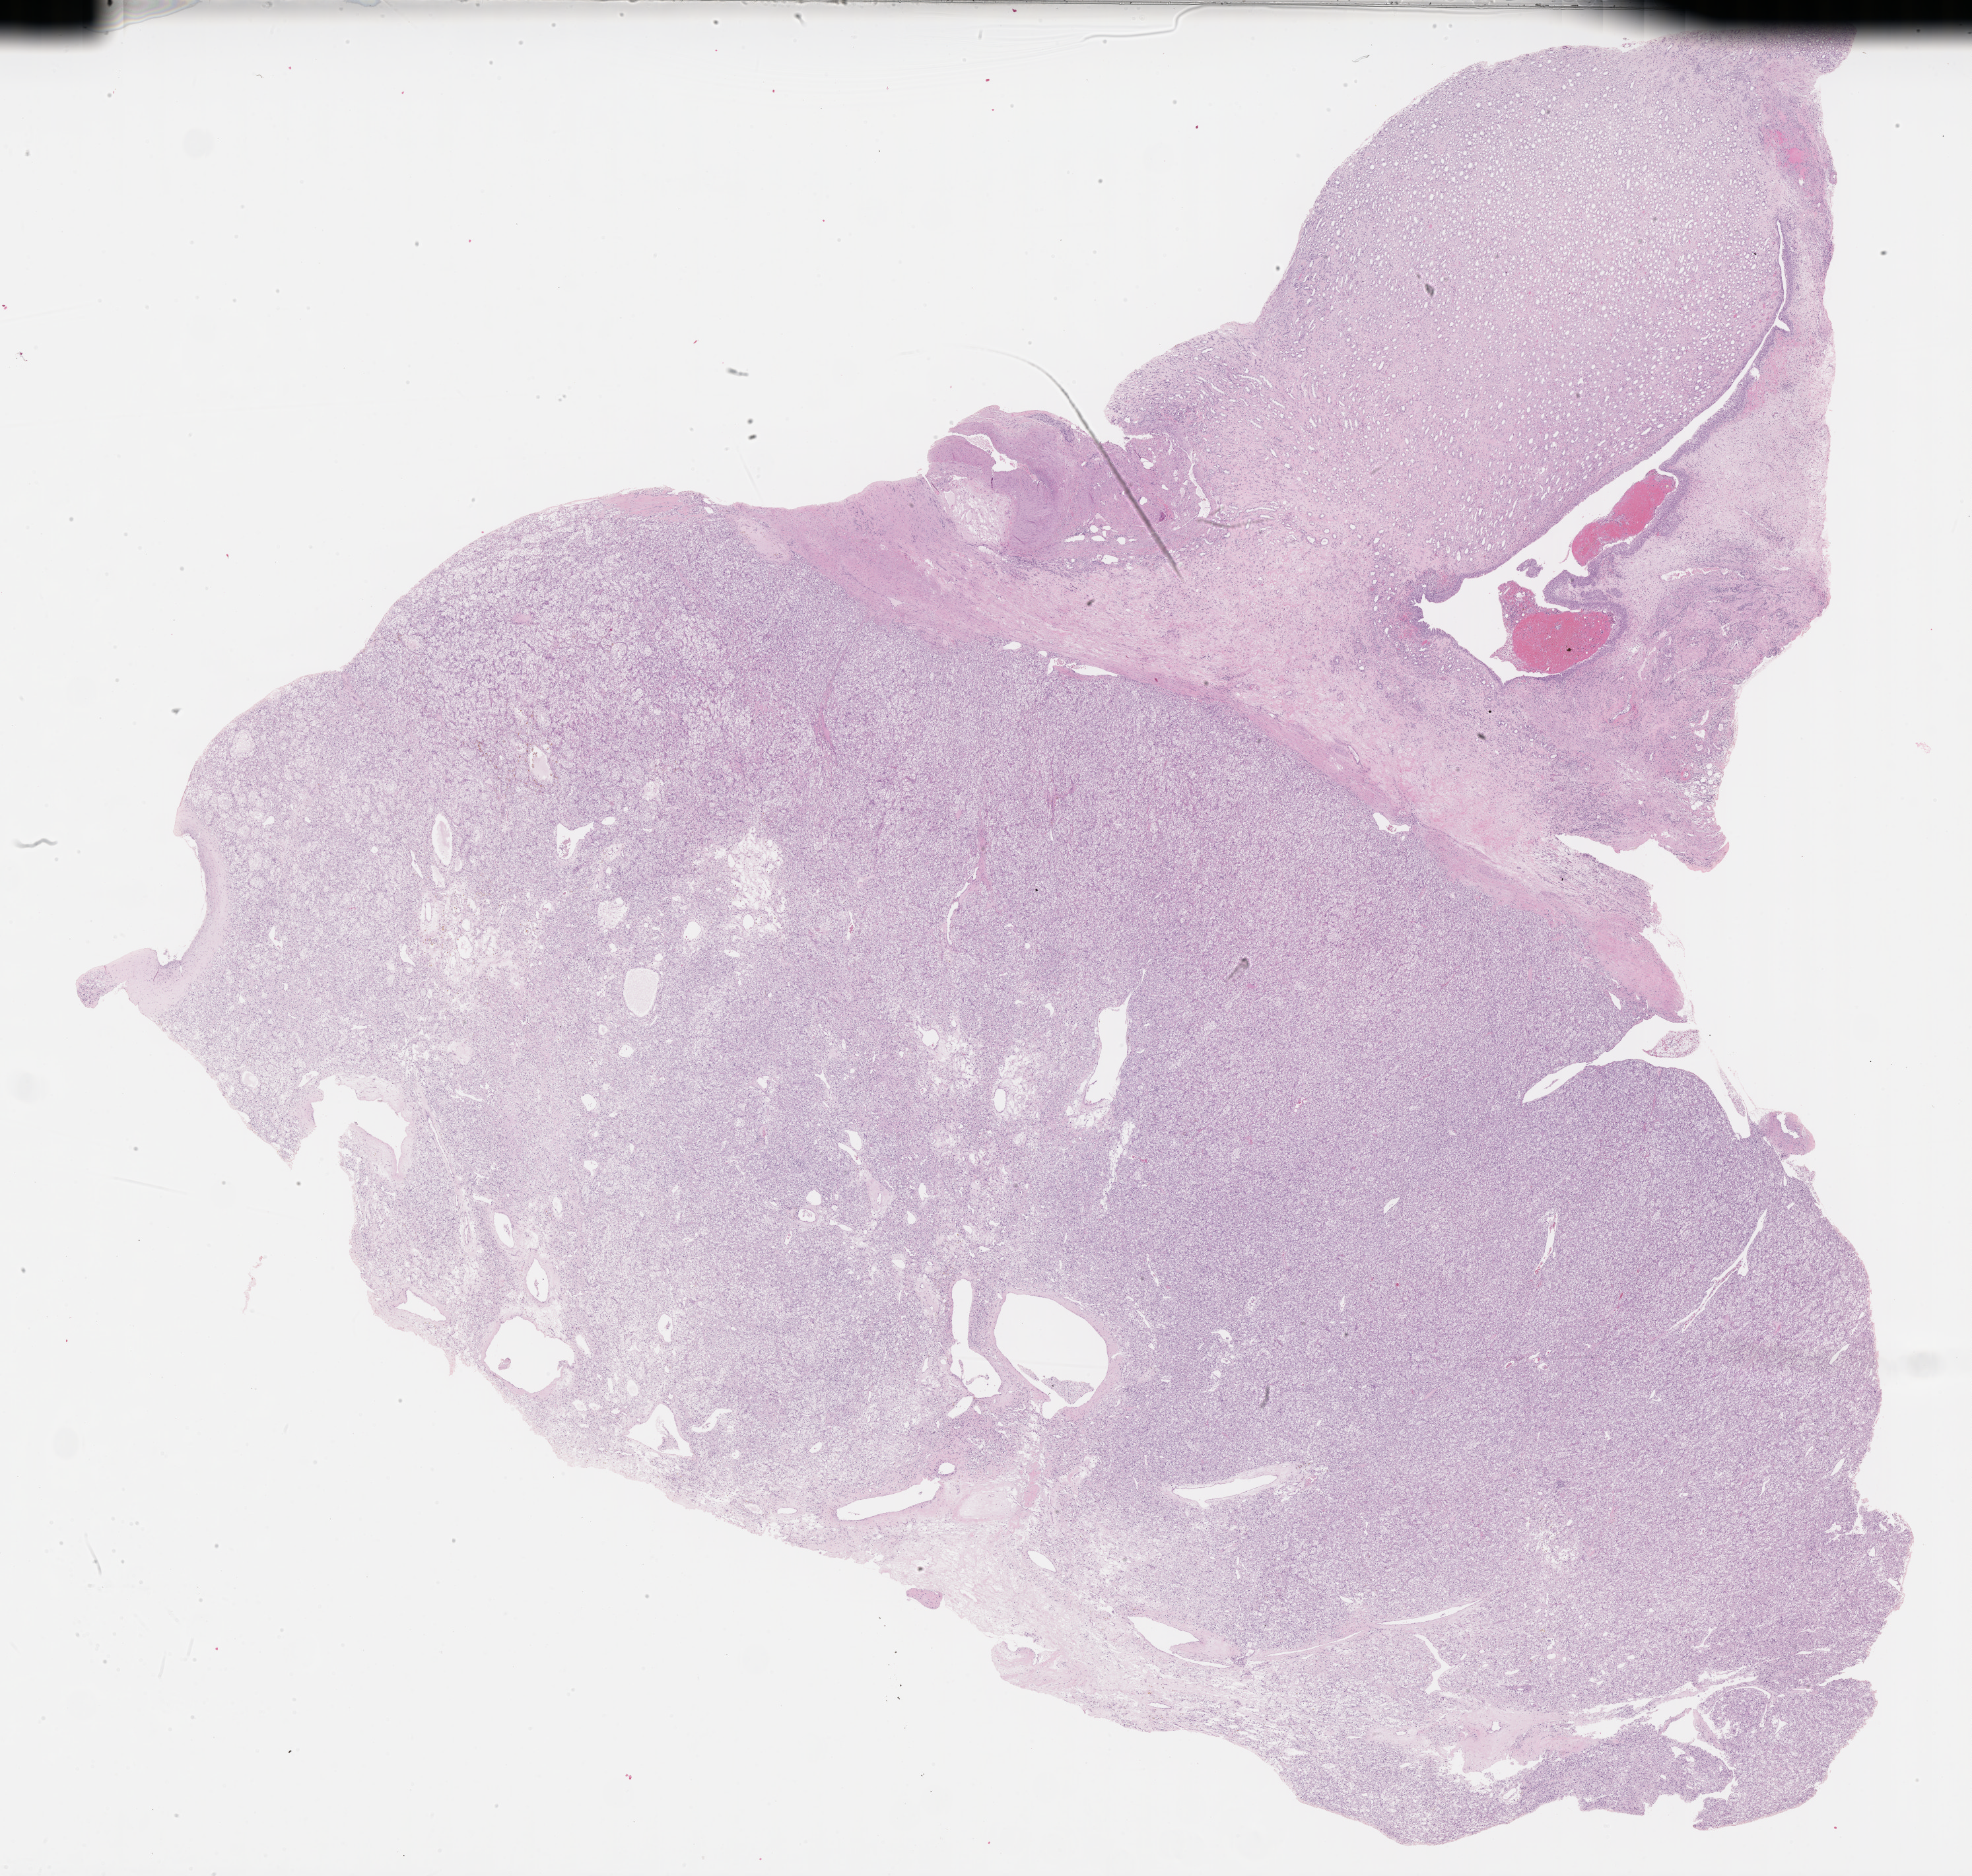
Whole-slide histology image, H&E-stained — low-resolution overview of the scanned area, about 24.2 x 23.0 mm (acquisition: 40x scan). FFPE section. Kidney, primary tumour sample. Male patient; age at initial diagnosis 62 years.
Histologic diagnosis: Clear cell adenocarcinoma, NOS.